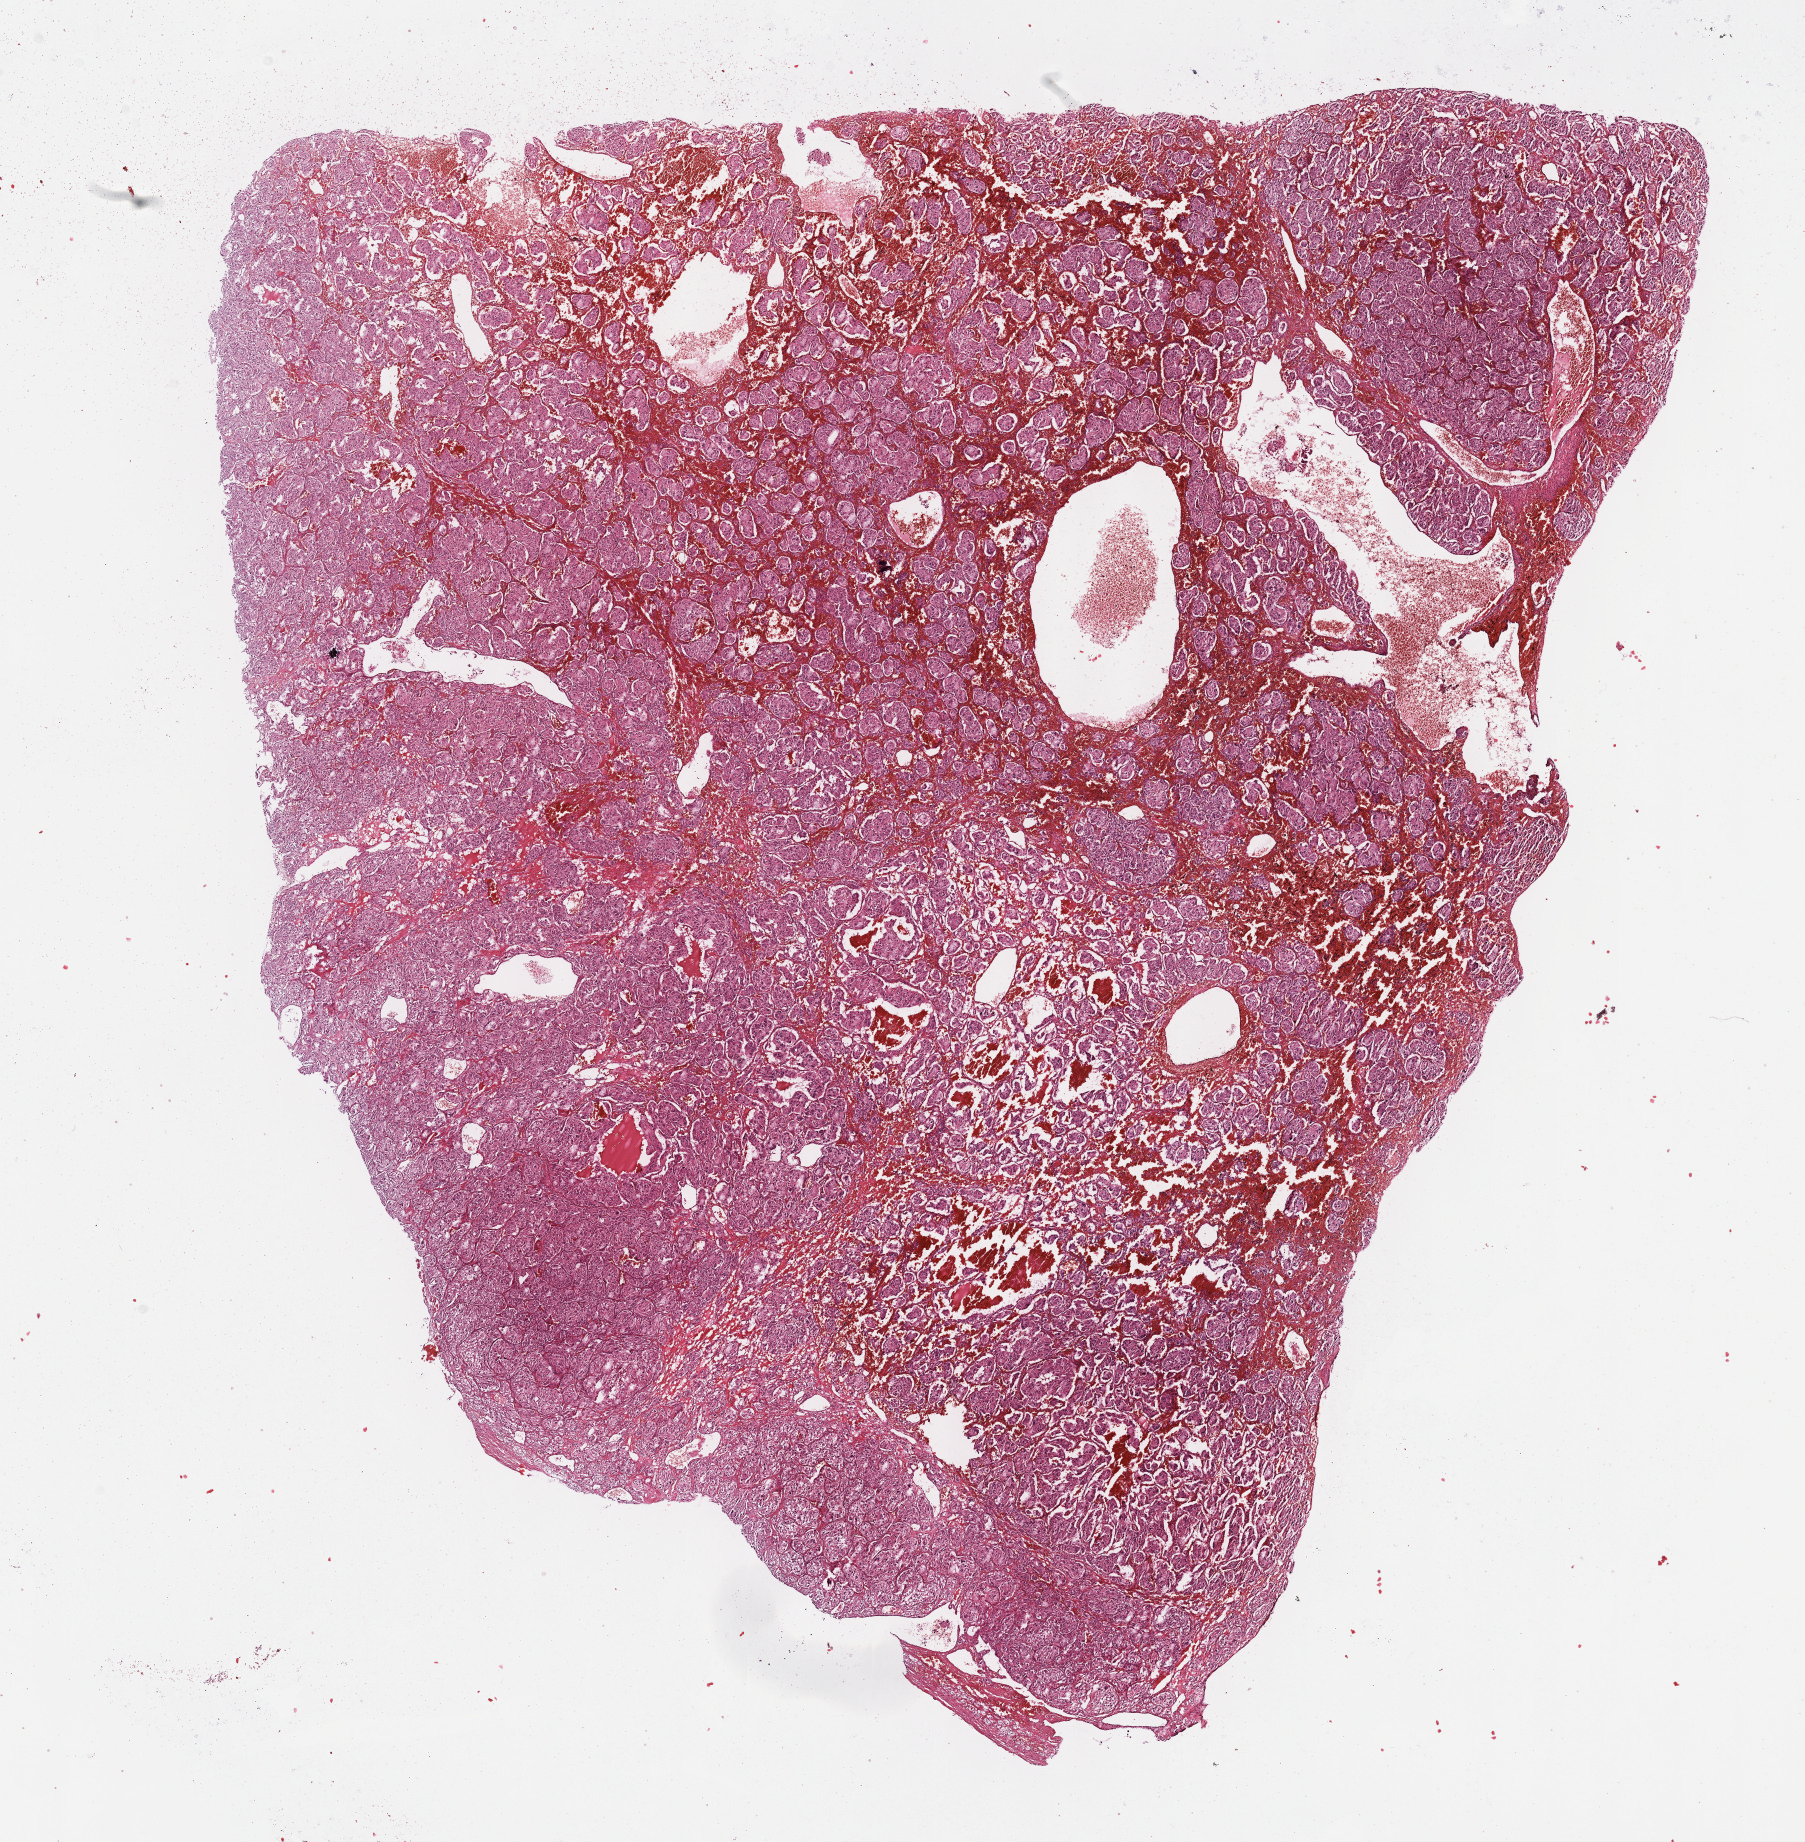
Whole-slide histology image, H&E, whole scanned area (about 14.6 x 14.9 mm, slide scanned at 40x) shown as a low-resolution overview; formalin-fixed paraffin-embedded (FFPE) diagnostic section; sample: primary tumour, adrenal gland. Female patient; age at initial diagnosis 25 years.
Laterality: left. Histologic diagnosis: Pheochromocytoma, NOS.